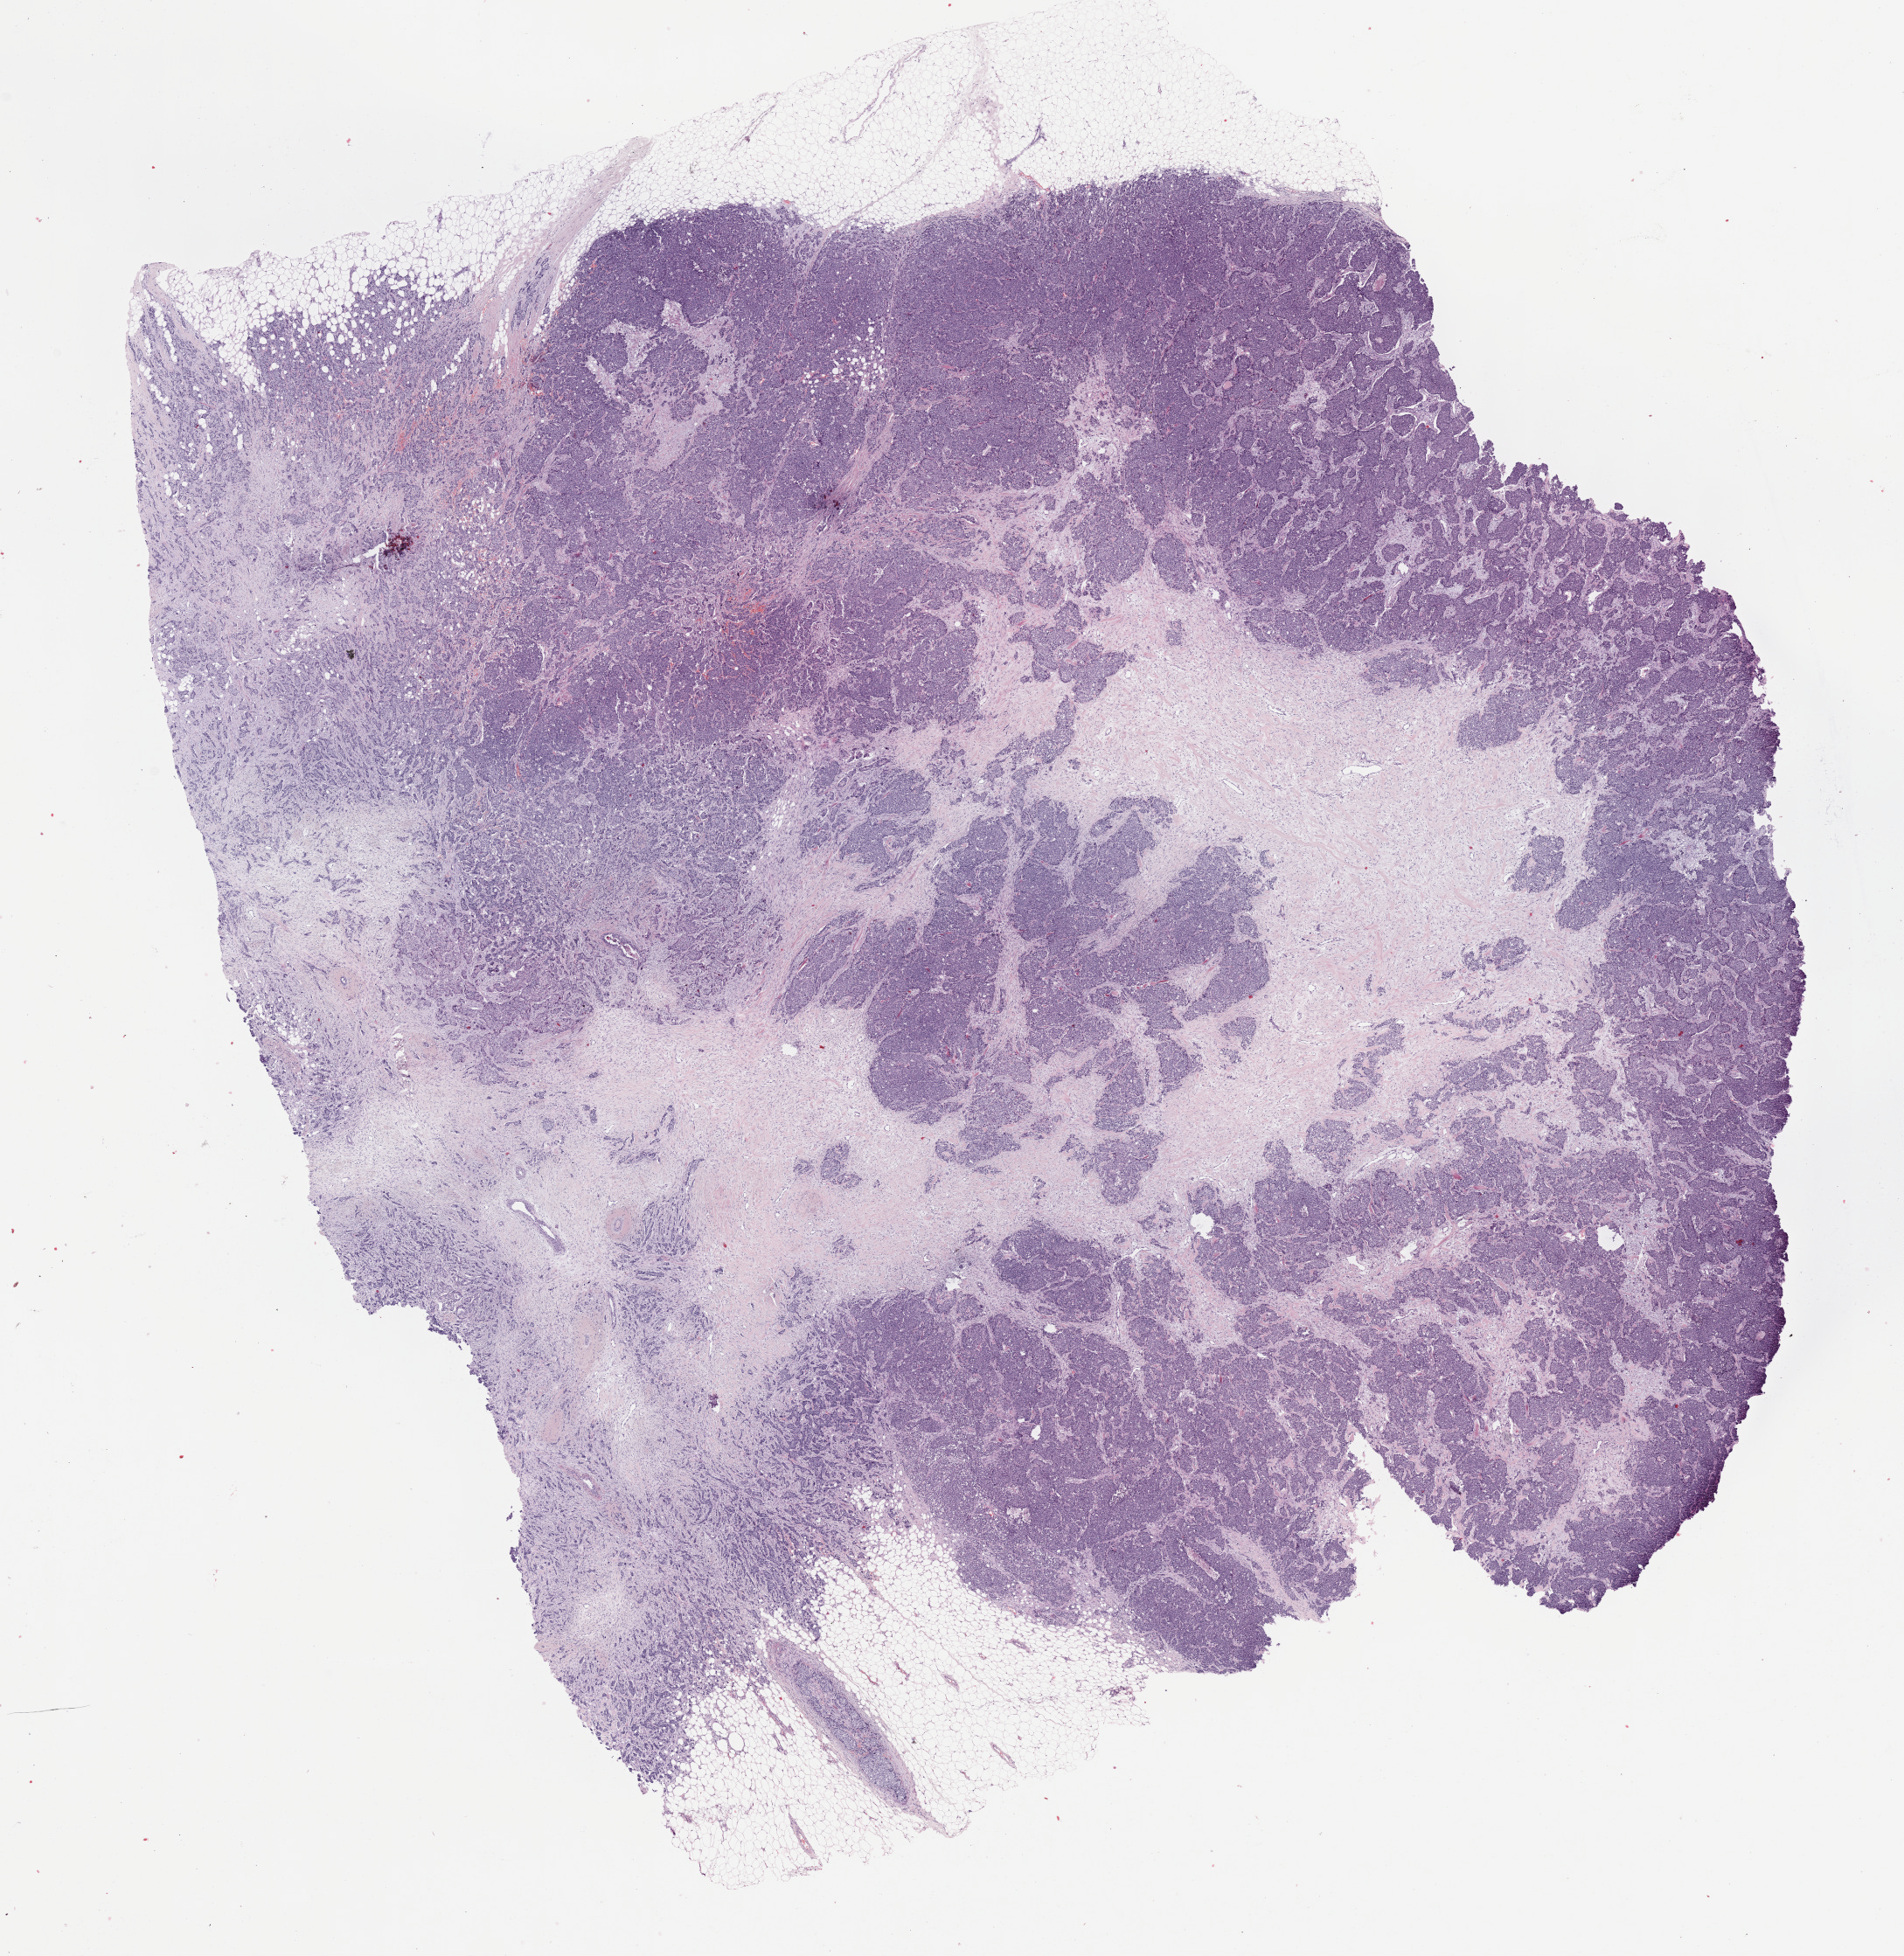
H&E-stained whole-slide image — whole scanned area (about 17.6 x 18.1 mm) shown as a low-resolution overview; FFPE section; sample: primary tumour, breast. Female, age 52 years at initial diagnosis.
- TNM: T1c N0 M0
- AJCC pathologic stage: IA
- laterality: right
- lymph nodes positive (case pathology): 0 of 6 examined
- histologic diagnosis: Infiltrating duct carcinoma, NOS